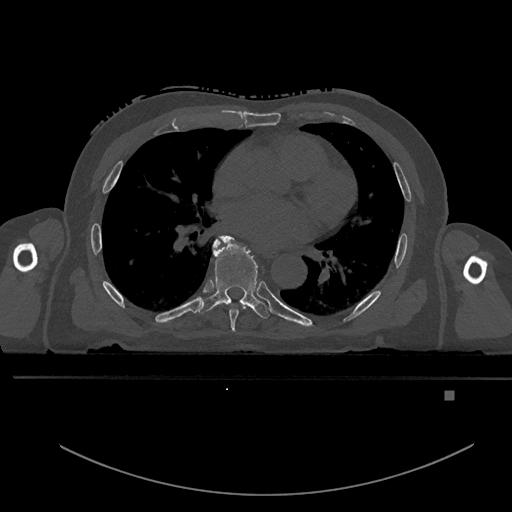
CT including the spine, one axial slice; position 272 of 969 along the scan axis; bone window (W 1800 / L 400 HU); 0.5 mm slice thickness; 512 × 512 image matrix, field of view 456 × 456 mm. Patient: male, 82 years. From the clinical record (not read from this slice): primary cancer: prostate; vertebrae with lytic lesions (as recorded): T11, T9, T8, T2.
Annotated regions visible in this slice (semi-automatic segmentation, software-assisted and operator-edited):
- T6 vertebra: bounding box <215,239,247,332> (left, top, right, bottom; pixels)
- T7 vertebra: <198,235,269,319>